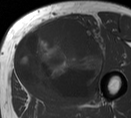
MRI of an extremity soft-tissue mass, one axial slice. Position 35 of 55 along the scan axis. MR volume resampled by the dataset authors to the PET/CT grid (not the native acquisition matrix). 3.27 mm slice thickness. 131 × 118 image matrix, field of view 128 × 115 mm. Male patient. From the clinical record (not read from this slice): histological type: pleiomorphic liposarcoma; grade: high; site of the primary tumour: left thigh.
Structures marked on this image (expert contour drawn on MRI and transferred to this co-registered scan by the dataset authors):
- gross tumour volume including surrounding oedema: box from (x=14, y=18) to (x=106, y=101) px
- gross tumour volume (mass): (x=14, y=18)–(x=103, y=101)